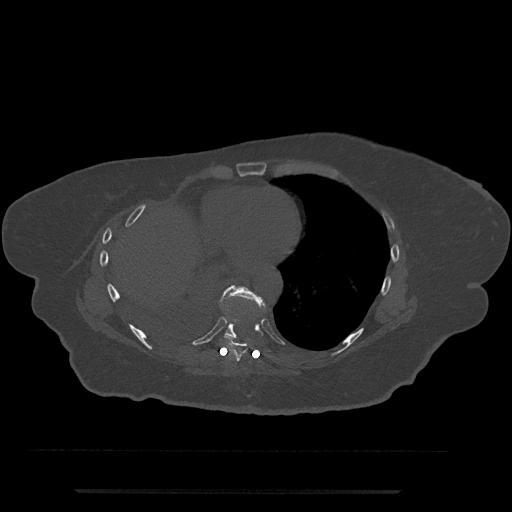
CT including the spine, one axial slice; slice 370 of 797 in the series (ordered by position); 120 kVp; bone window (W 1800 / L 400 HU); 0.5 mm slice thickness; 512 × 512 image matrix, field of view 440 × 440 mm. Patient: female, 51 years. From the clinical record (not read from this slice): primary cancer: neuro; vertebrae with lytic lesions (as recorded): T8.
Annotated regions visible in this slice (semi-automatically segmented with operator editing):
- T8 vertebra: bounding box (x1, y1, x2, y2) in pixels: (223, 333, 248, 361)
- T9 vertebra: (218, 285, 266, 339)